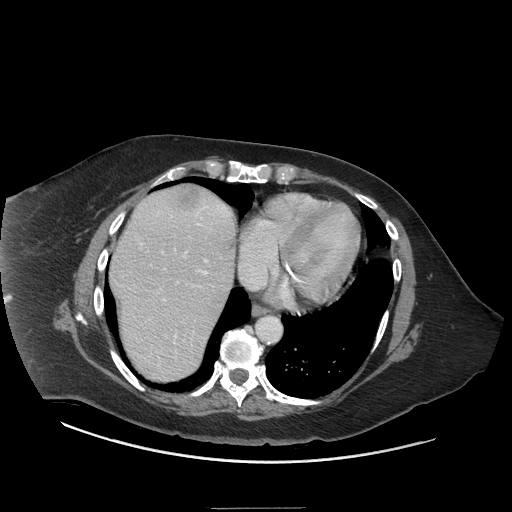
Contrast-enhanced abdominal CT (liver protocol), one axial slice. Position 63 of 81 along the scan axis. Reconstruction kernel STANDARD. Soft-tissue window (W 400 / L 40 HU). 512 × 512 image matrix, field of view 440 × 440 mm. Case-level facts recorded for this patient, not image findings: diagnosis: hepatocellular carcinoma (patient treated with transarterial chemoembolisation; whether this scan precedes or follows treatment is not stated here); TNM stage (as recorded): Stage-II; Child-Pugh class: A.
Outlined on this slice (semi-automatic segmentation, software-assisted and operator-edited):
- abdominal aorta: bounding box <257,317,281,343> (left, top, right, bottom; pixels)
- liver parenchyma outside the tumour (the mass and vessels are separate outlines, so this box may not span the whole liver): <110,184,234,380>
- mass: <172,185,201,208>
- liver vessels: <128,204,230,367>